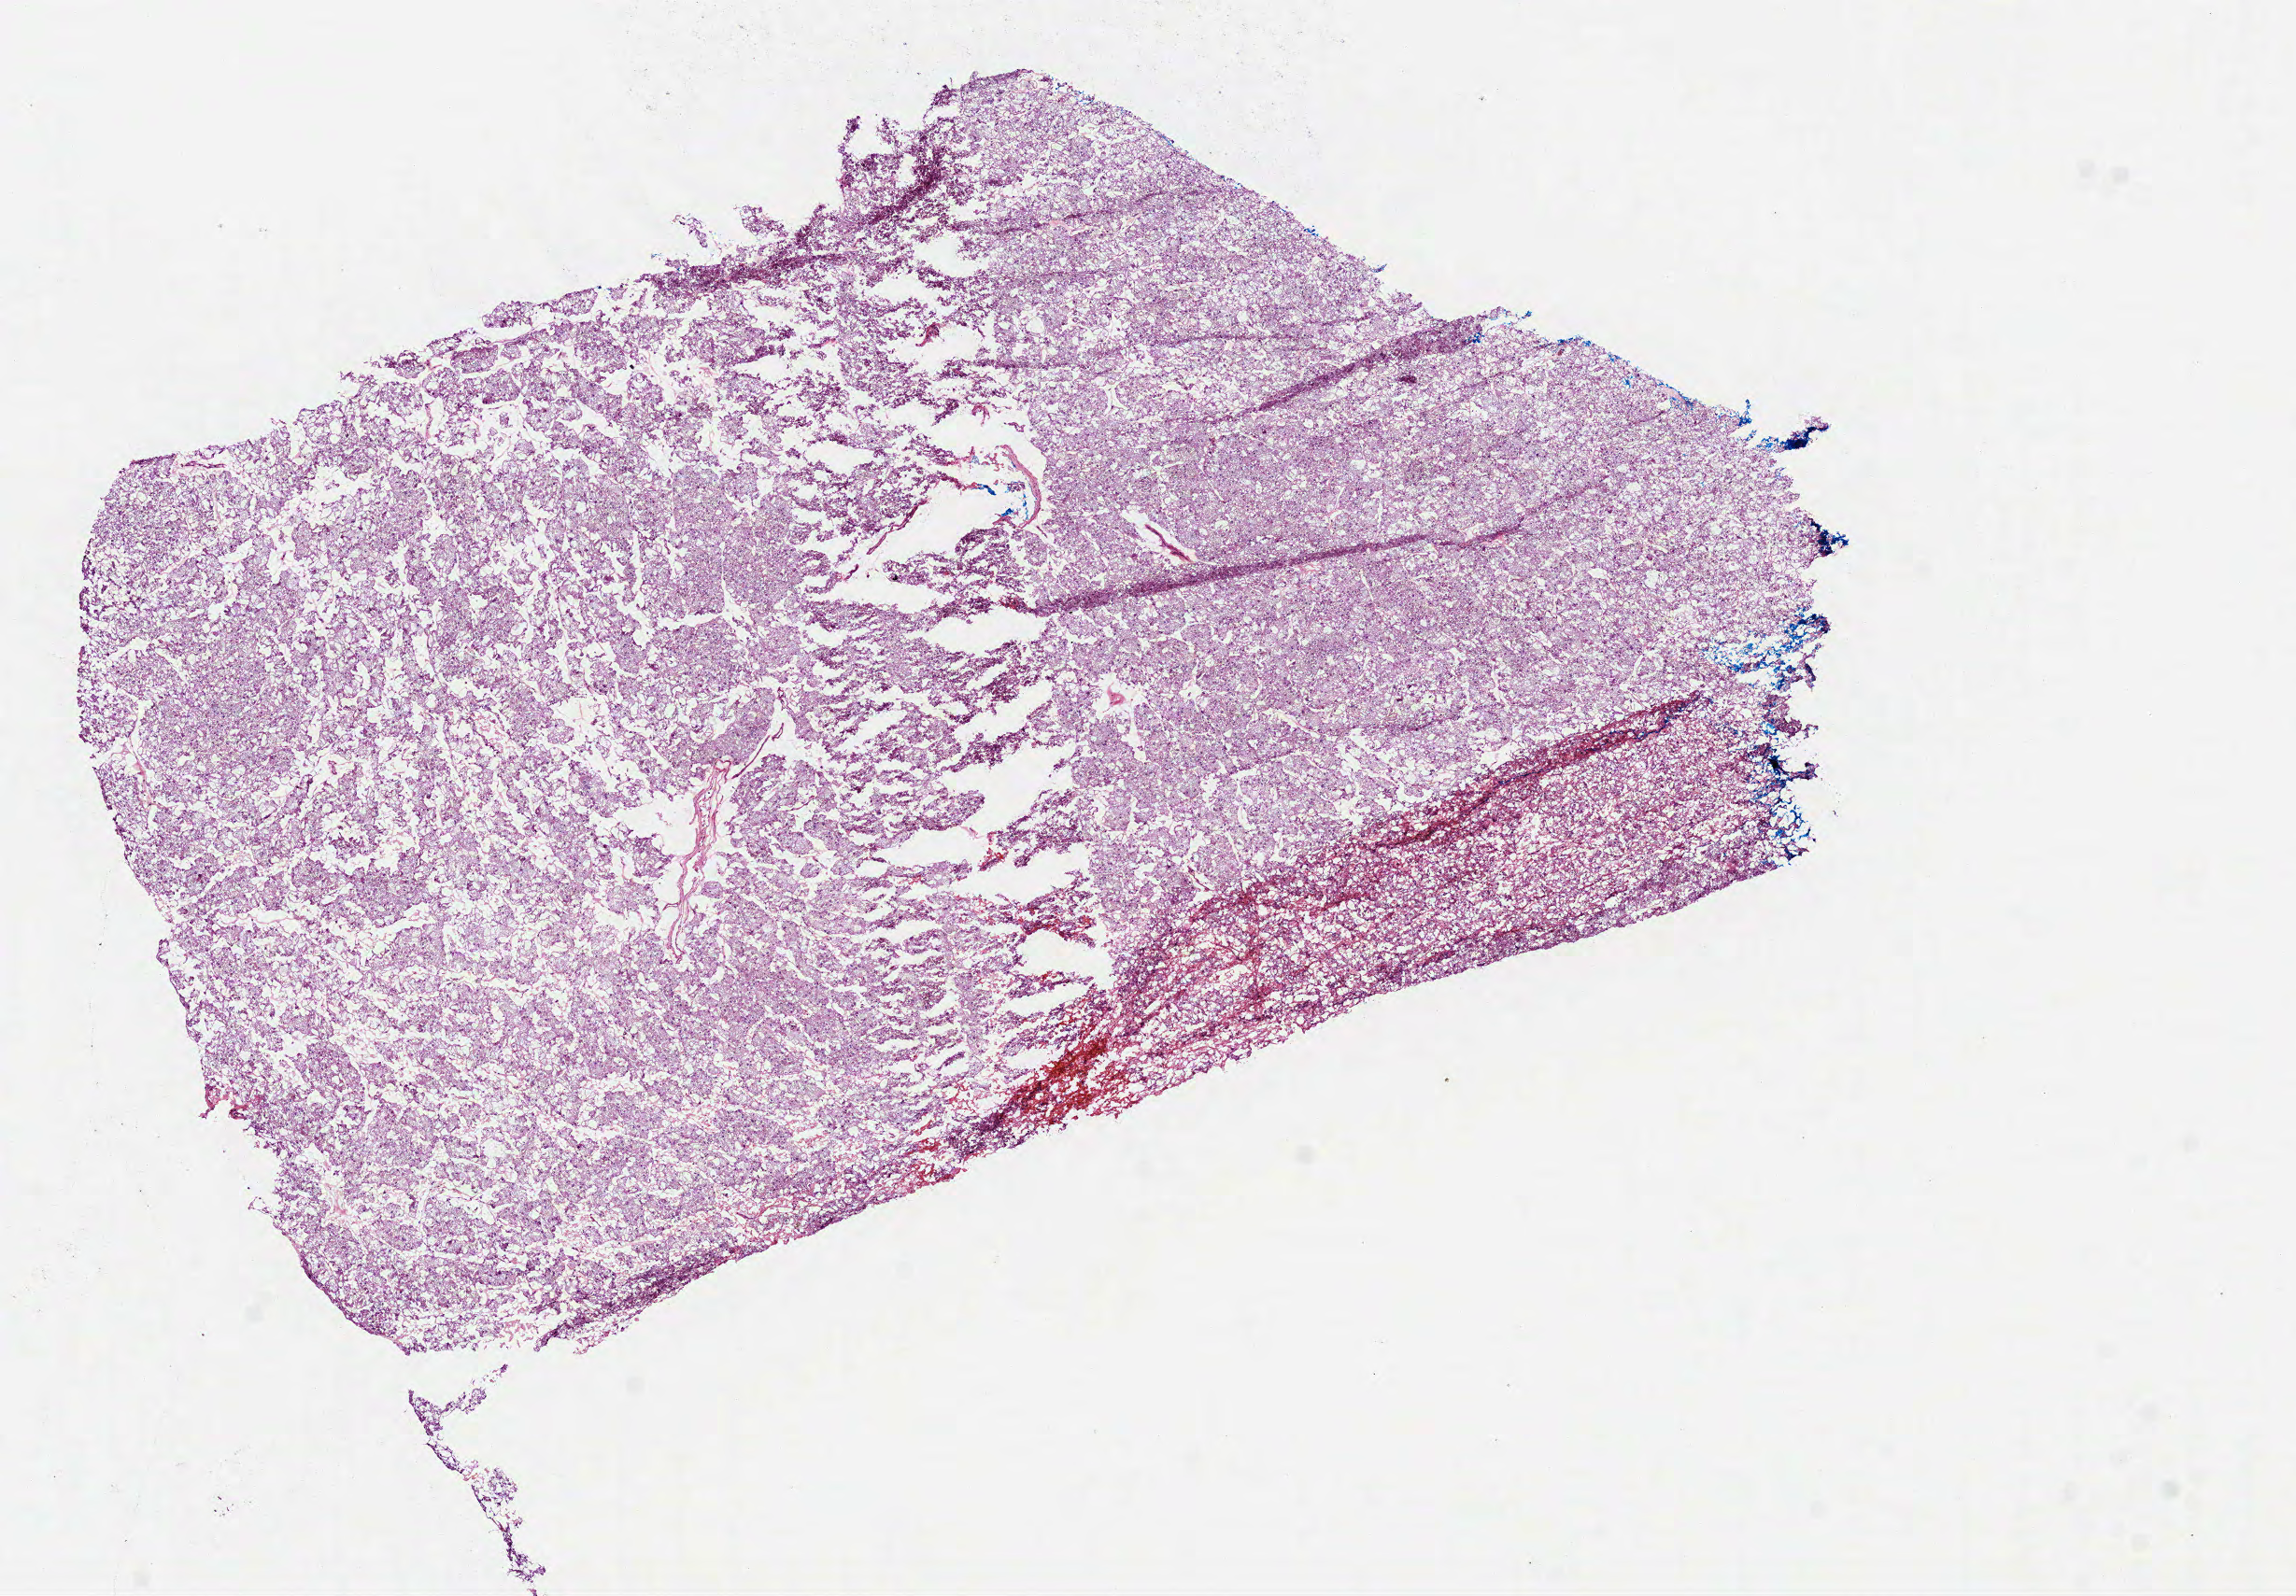
Digitized Hematoxylin and eosin (H&E) stained tissue section (whole slide), shown as a low-resolution overview of the whole scanned area (about 9.9 x 6.9 mm, from a 40x scan), frozen section from the top of the tissue portion, kidney, primary tumour sample. Female, age 79 years at initial diagnosis. Composition of this section per pathologist review: tumour cells 85%, tumour nuclei 90%, normal cells 0%, stromal cells 14%, necrosis 1%. Inflammatory infiltration, as recorded: lymphocyte infiltration 3%, monocyte infiltration 0%, neutrophil infiltration 0%.
- pathologic diagnosis: Renal cell carcinoma, chromophobe type
- laterality: right
- AJCC pathologic stage: I